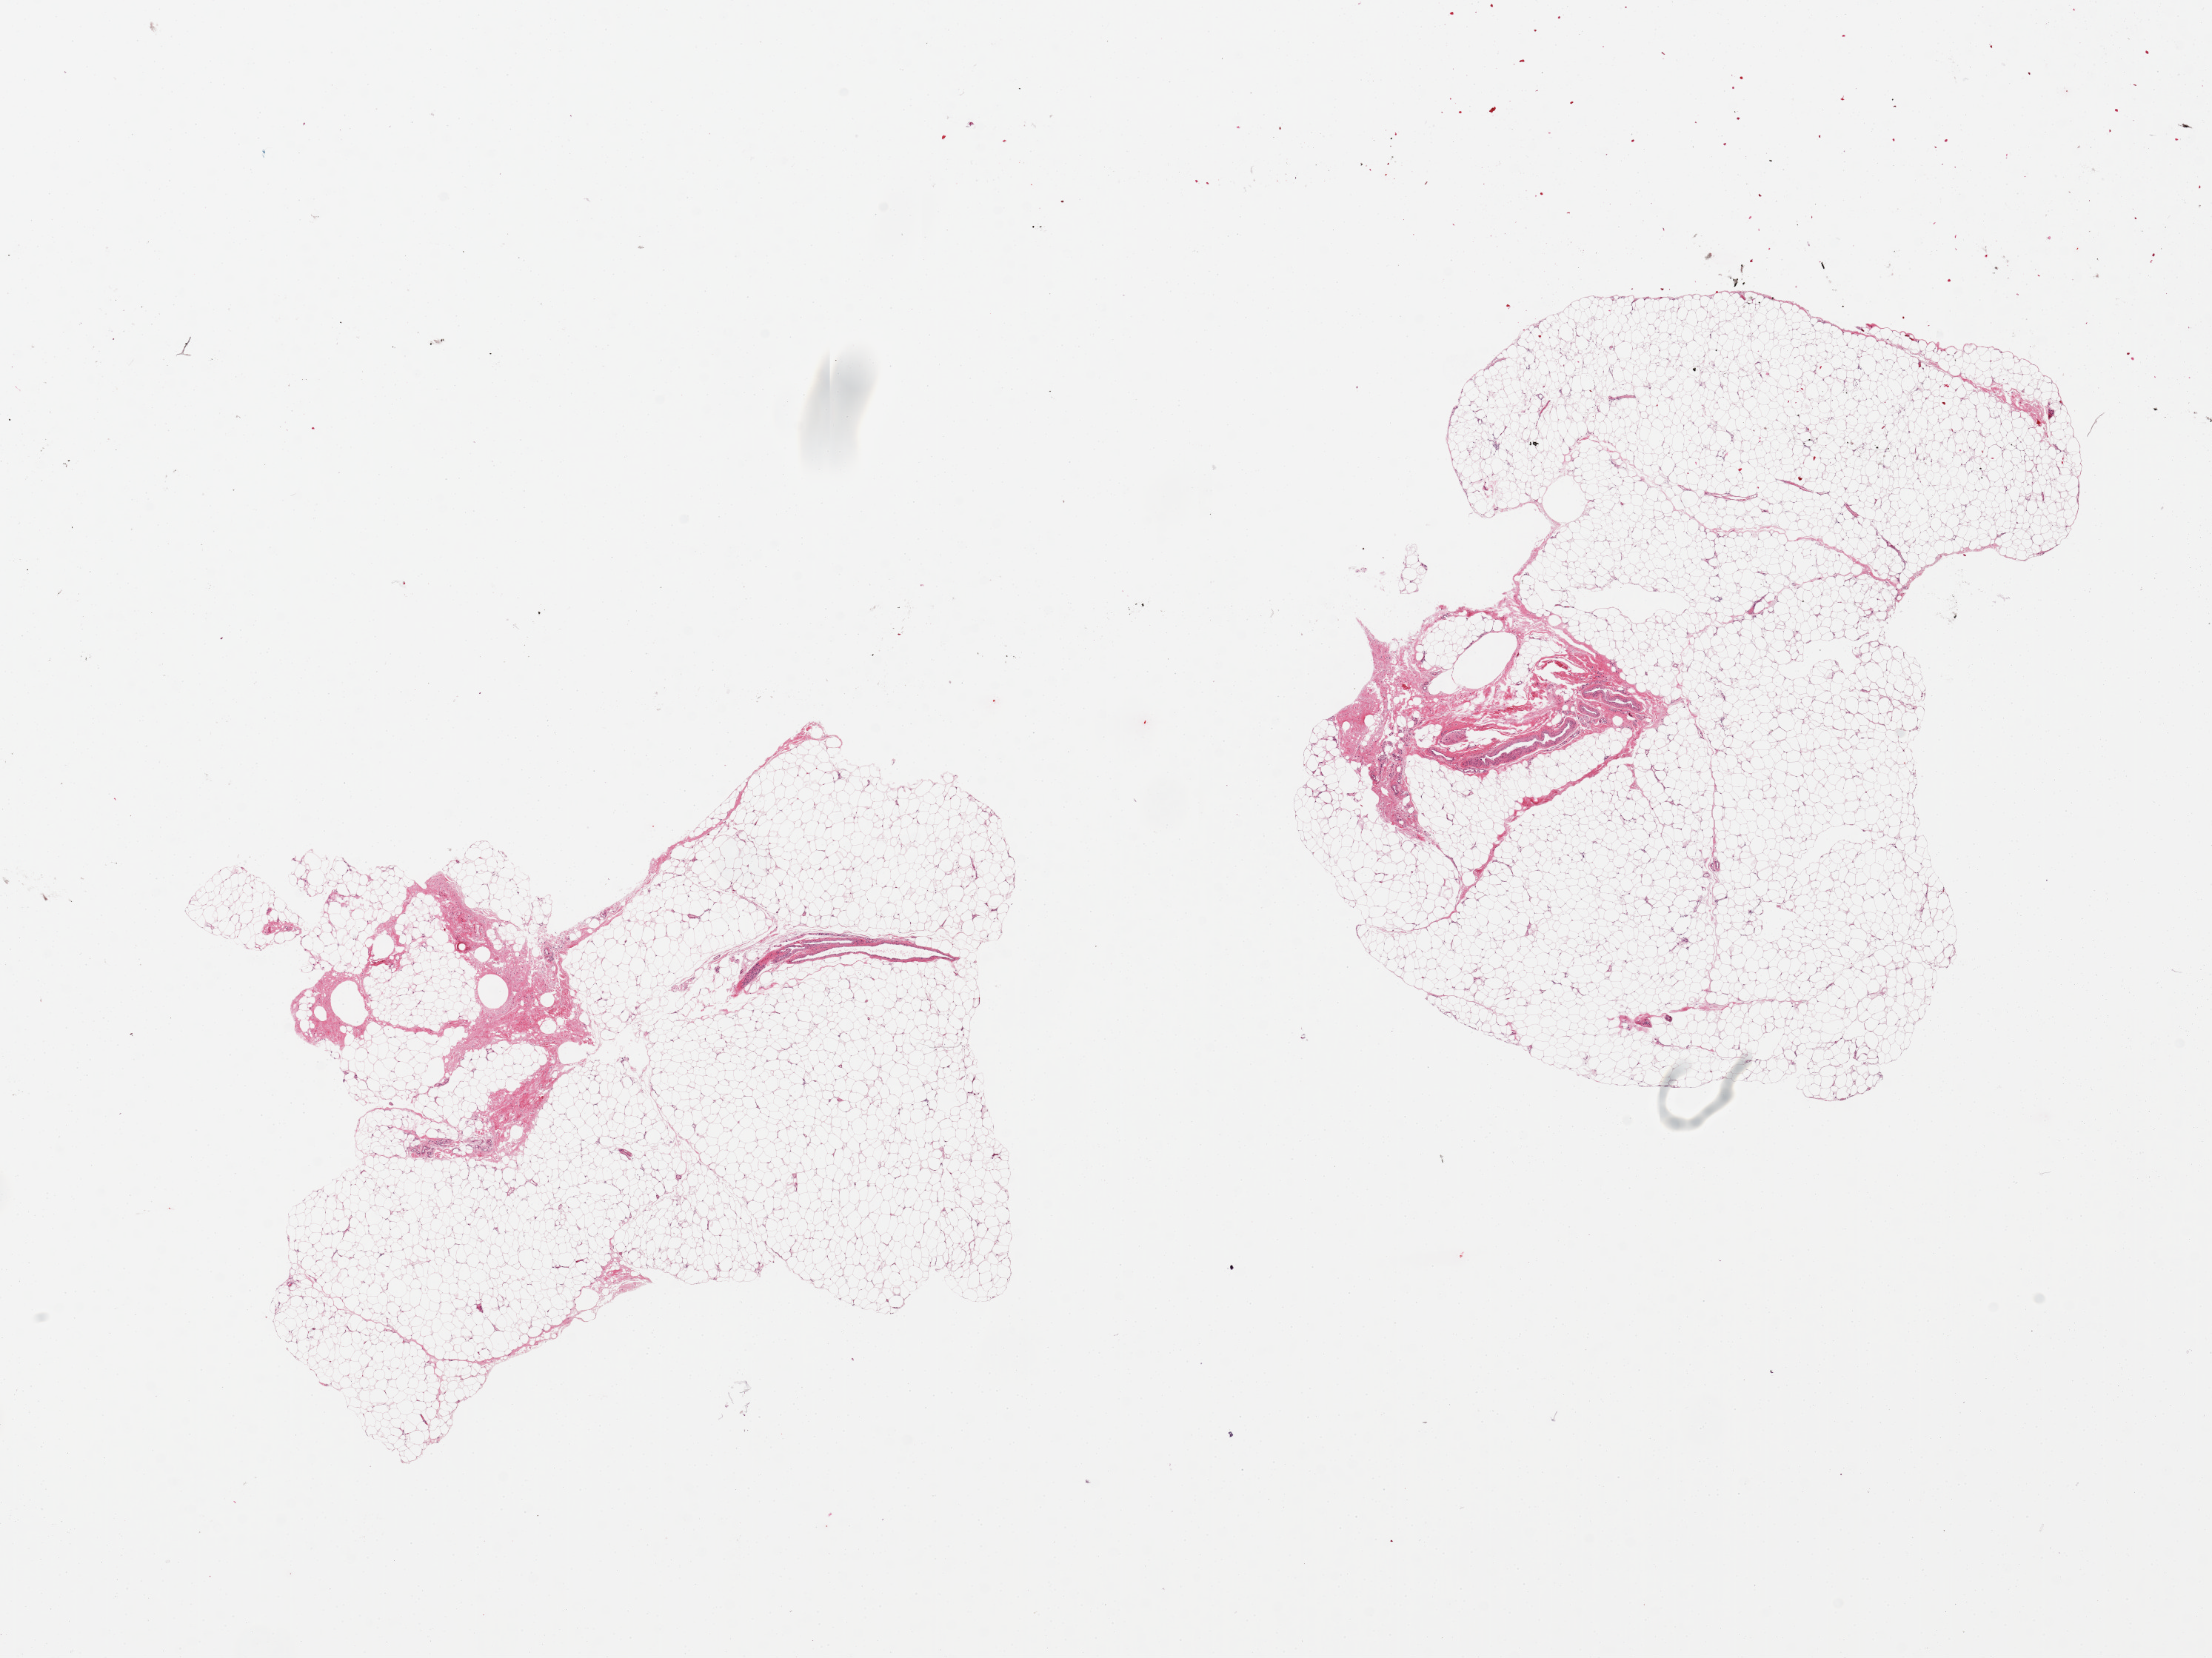
Whole-slide image, hematoxylin and eosin (H&E) stain, a low-resolution overview of the entire scanned area, about 23.6 x 17.7 mm (from a 20x scan). PAXgene-fixed, paraffin-embedded tissue. Section of adipose tissue (target tissue). Tissue donor sample. Donor: female.
• reviewer comment on this tissue sample: 2 pieces, ~10% fibrous tissue